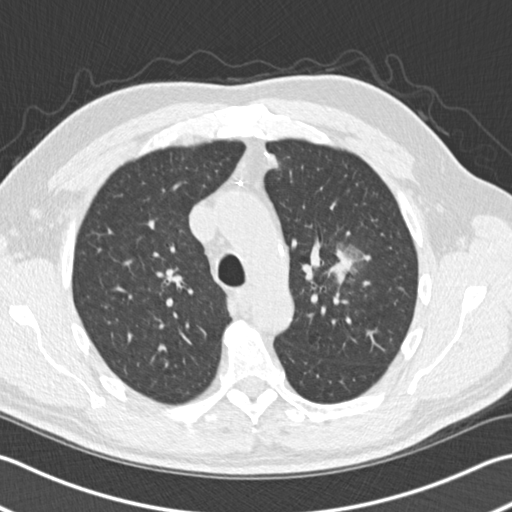
Low-dose screening chest CT, one axial slice. Slice 111 of 153 in the series (ordered by position). Lung window (W 1500 / L -600 HU). 512 × 512 image matrix, field of view 346 × 346 mm.
Structures marked on this image (manually delineated by an expert):
- lesion 1 (tumor, upper lobe of left lung): bounding box [x1, y1, x2, y2] px = [330, 252, 353, 282]